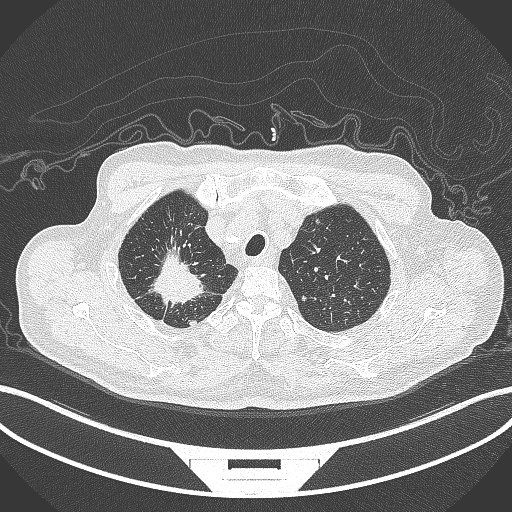
Chest CT, one axial slice. Position 325 of 407 along the scan axis. Reconstruction kernel B70f. 120 kVp. Lung window (W 1500 / L -600 HU). 1 mm slice thickness. 512 × 512 image matrix, field of view 400 × 400 mm. Male patient, age 69 years. Case-level facts recorded for this patient, not image findings: clinical TNM (as recorded): T1c N1 M1.
Annotated regions visible in this slice (rectangle marked by the reading radiologist):
- lung tumour (recorded histology: adenocarcinoma): box from (x=144, y=245) to (x=205, y=305) px